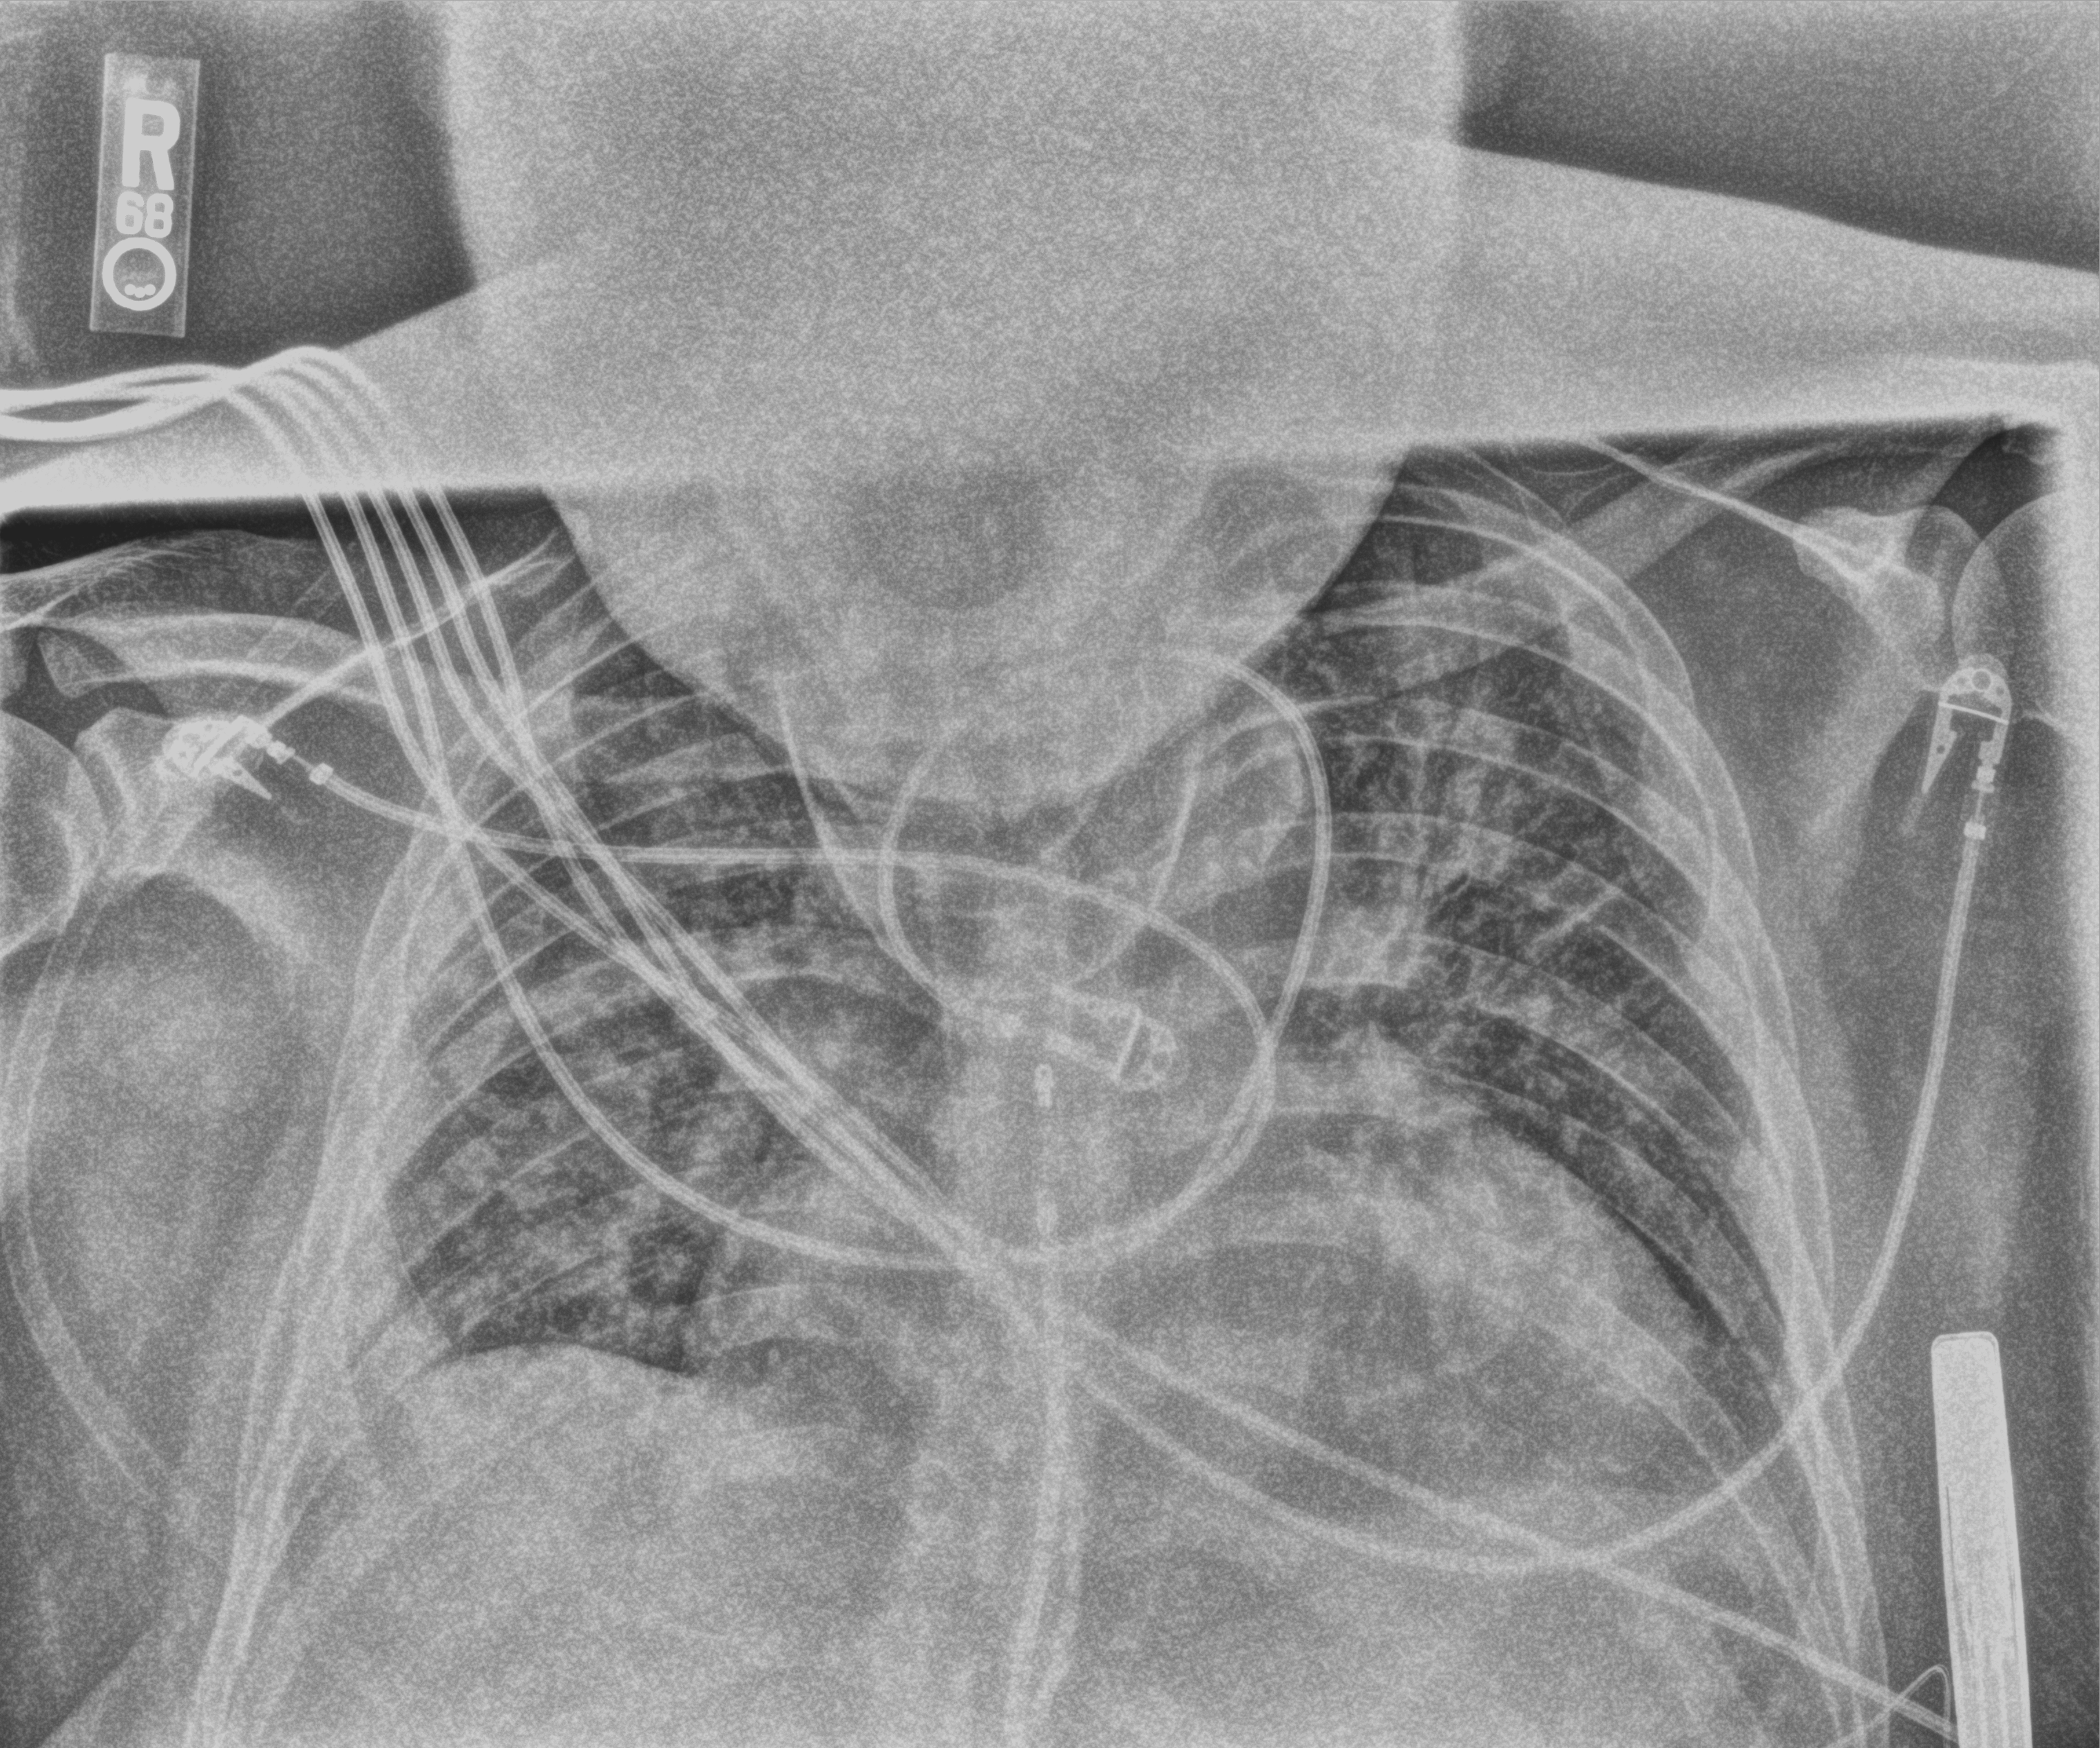
Chest X-ray (portable). Male patient hospitalised with COVID-19, age 18–59 years.
Admission-level facts for this patient (not findings on this image; timing relative to this image not recorded):
- admitted to intensive care during this hospital stay: no